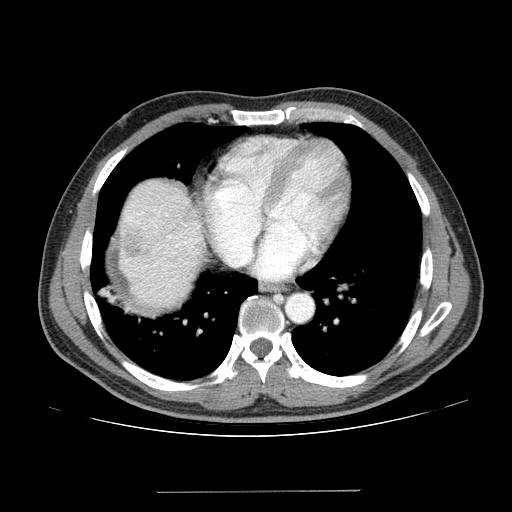
Contrast-enhanced abdominal CT (liver protocol), one axial slice; position 122 of 131 along the scan axis; reconstruction kernel STANDARD; 100 kVp; one of 2 acquisitions stored at this slice position; soft-tissue window (W 400 / L 40 HU); 2.5 mm slice thickness; 512 × 512 image matrix. Case-level facts recorded for this patient, not image findings: diagnosis: hepatocellular carcinoma (patient treated with transarterial chemoembolisation; whether this scan precedes or follows treatment is not stated here); TNM stage (as recorded): Stage-I; Child-Pugh class: A; tumour differentiation: poorly differentiated; tumour nodularity: uninodular.
Outlined on this slice (semi-automatically segmented with operator editing):
- liver parenchyma outside the tumour (the mass and vessels are separate outlines, so this box may not span the whole liver): box from (x=118, y=180) to (x=204, y=308) px
- mass: (x=117, y=227)–(x=144, y=259)
- liver vessels: (x=124, y=213)–(x=199, y=271)